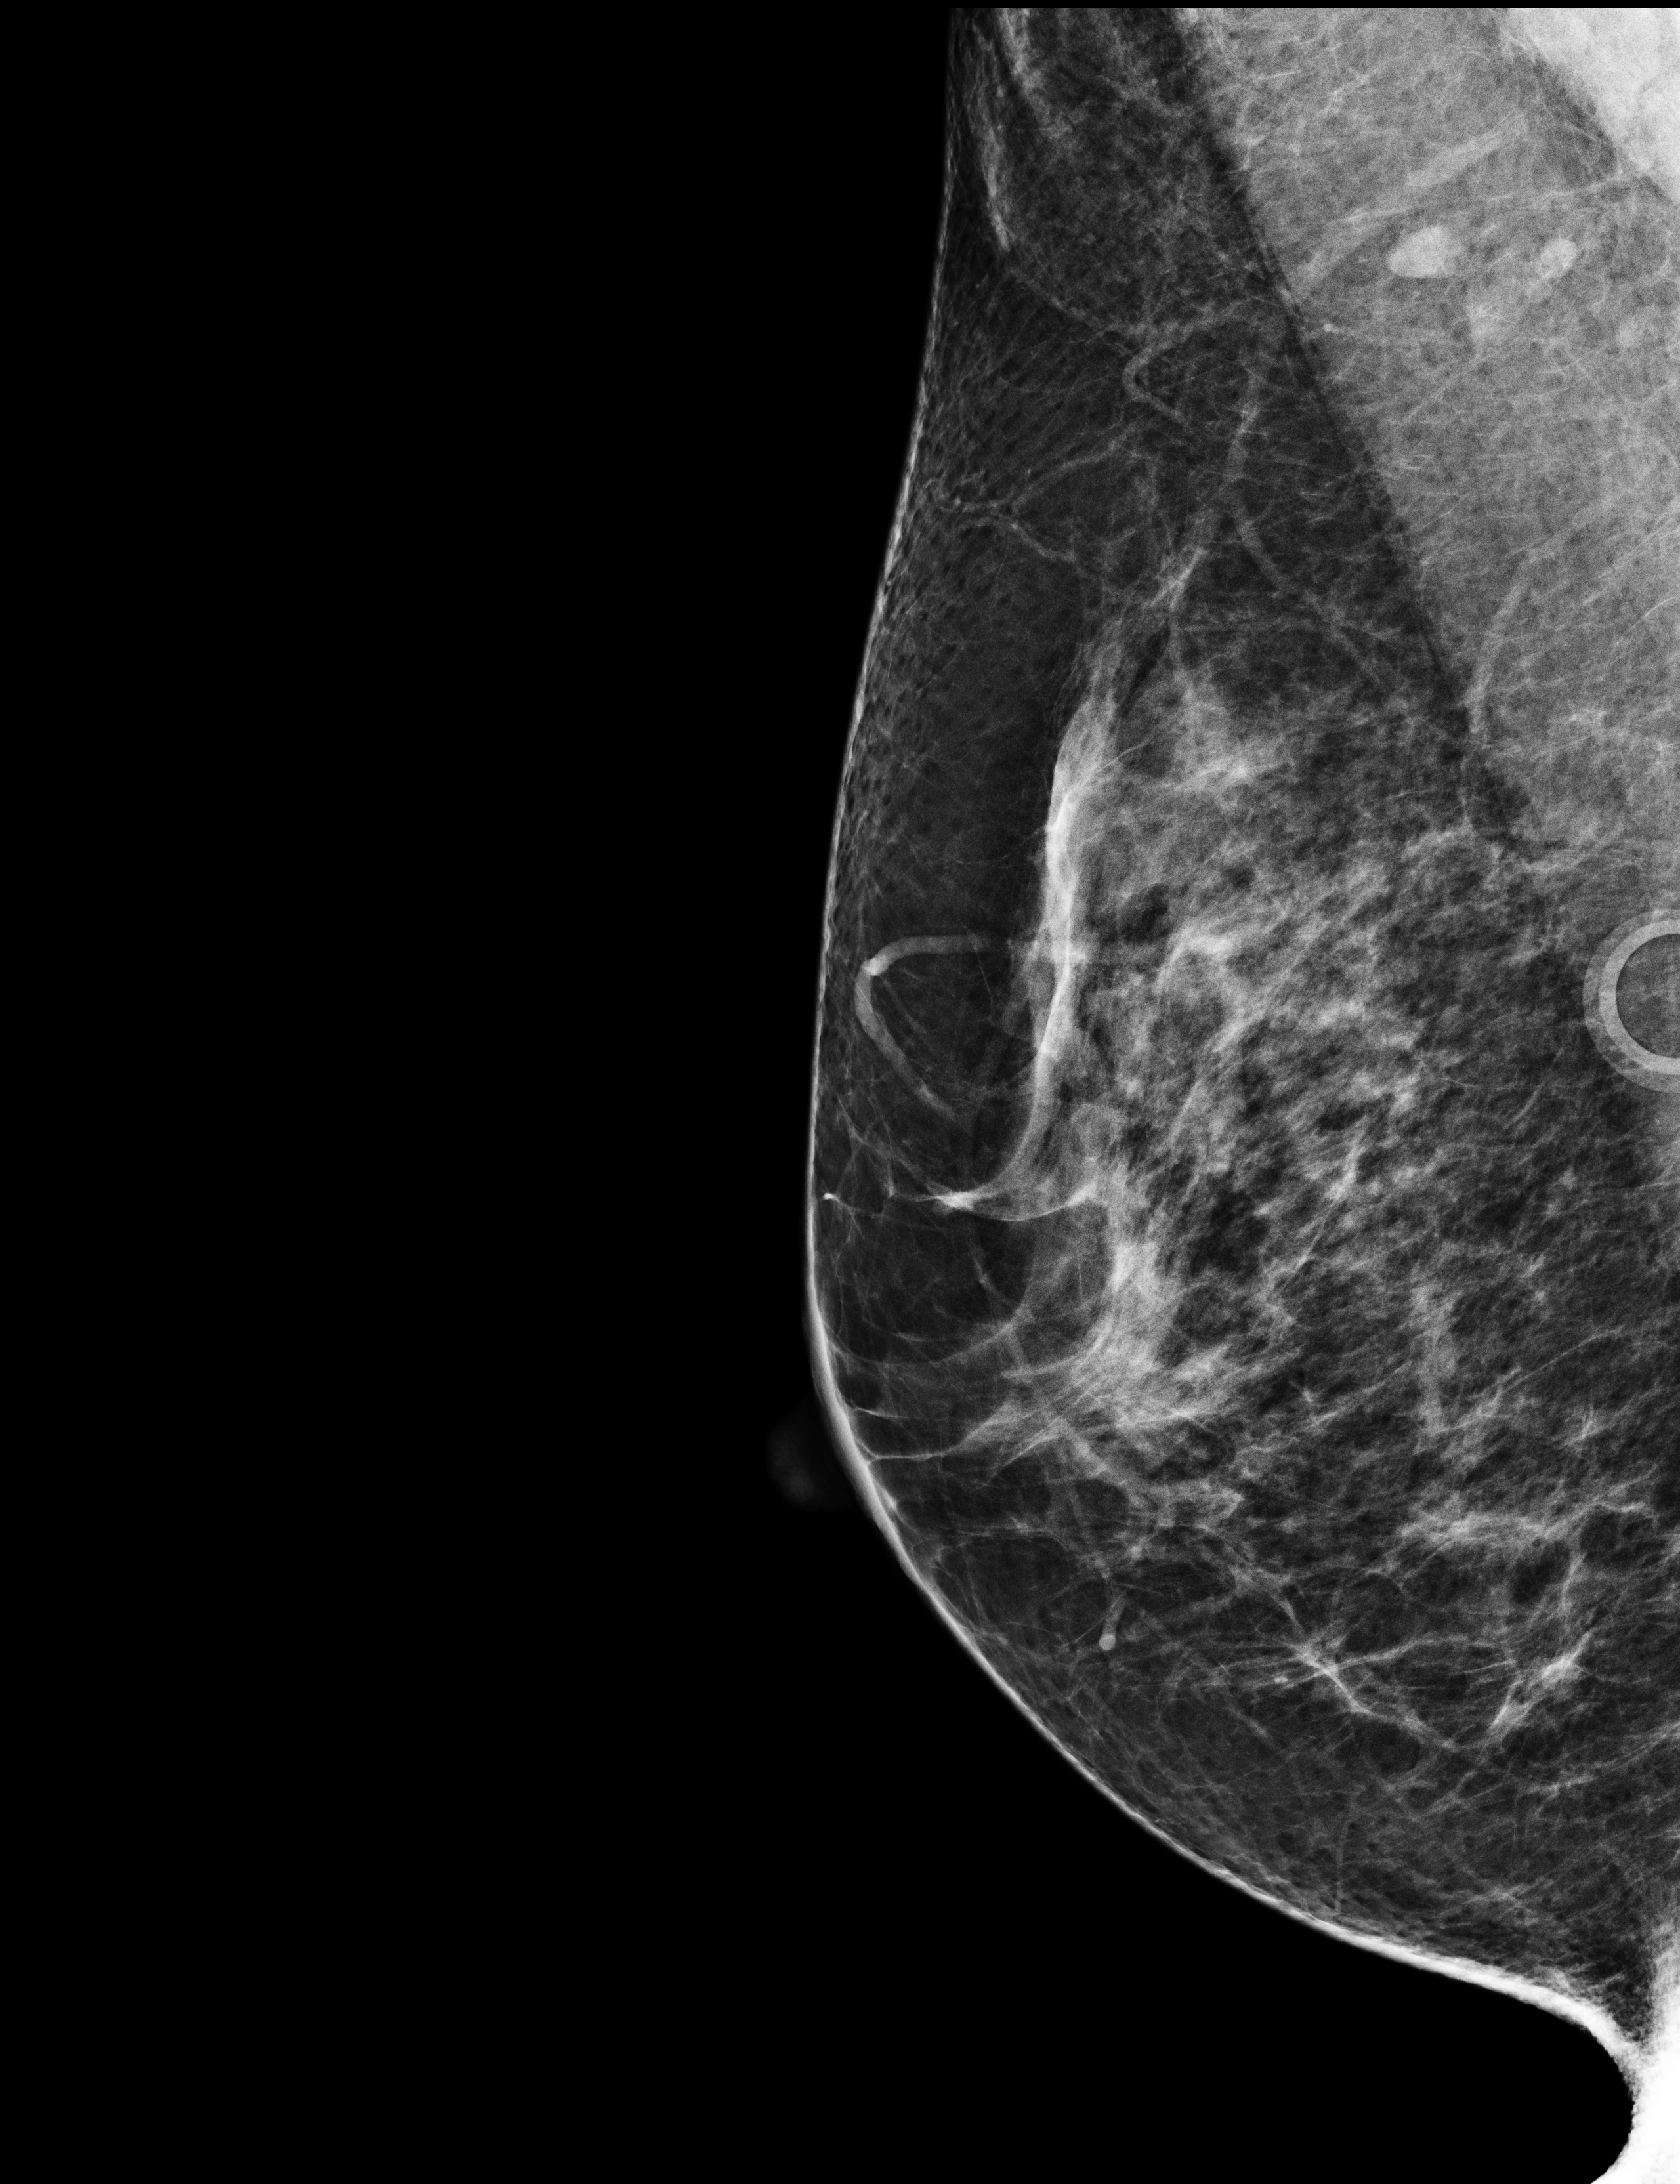
Full-field digital mammogram (FFDM), right breast, medio-lateral oblique projection, annual screening mammography examination, system: Selenia Dimensions. Female patient, age 53 years.
Breast density at the screening exam (both breasts): heterogeneously dense (BI-RADS density category c). Final BI-RADS assessment for this screening round (tomosynthesis exam, both breasts): category 1. Recall: no recall after this screen.